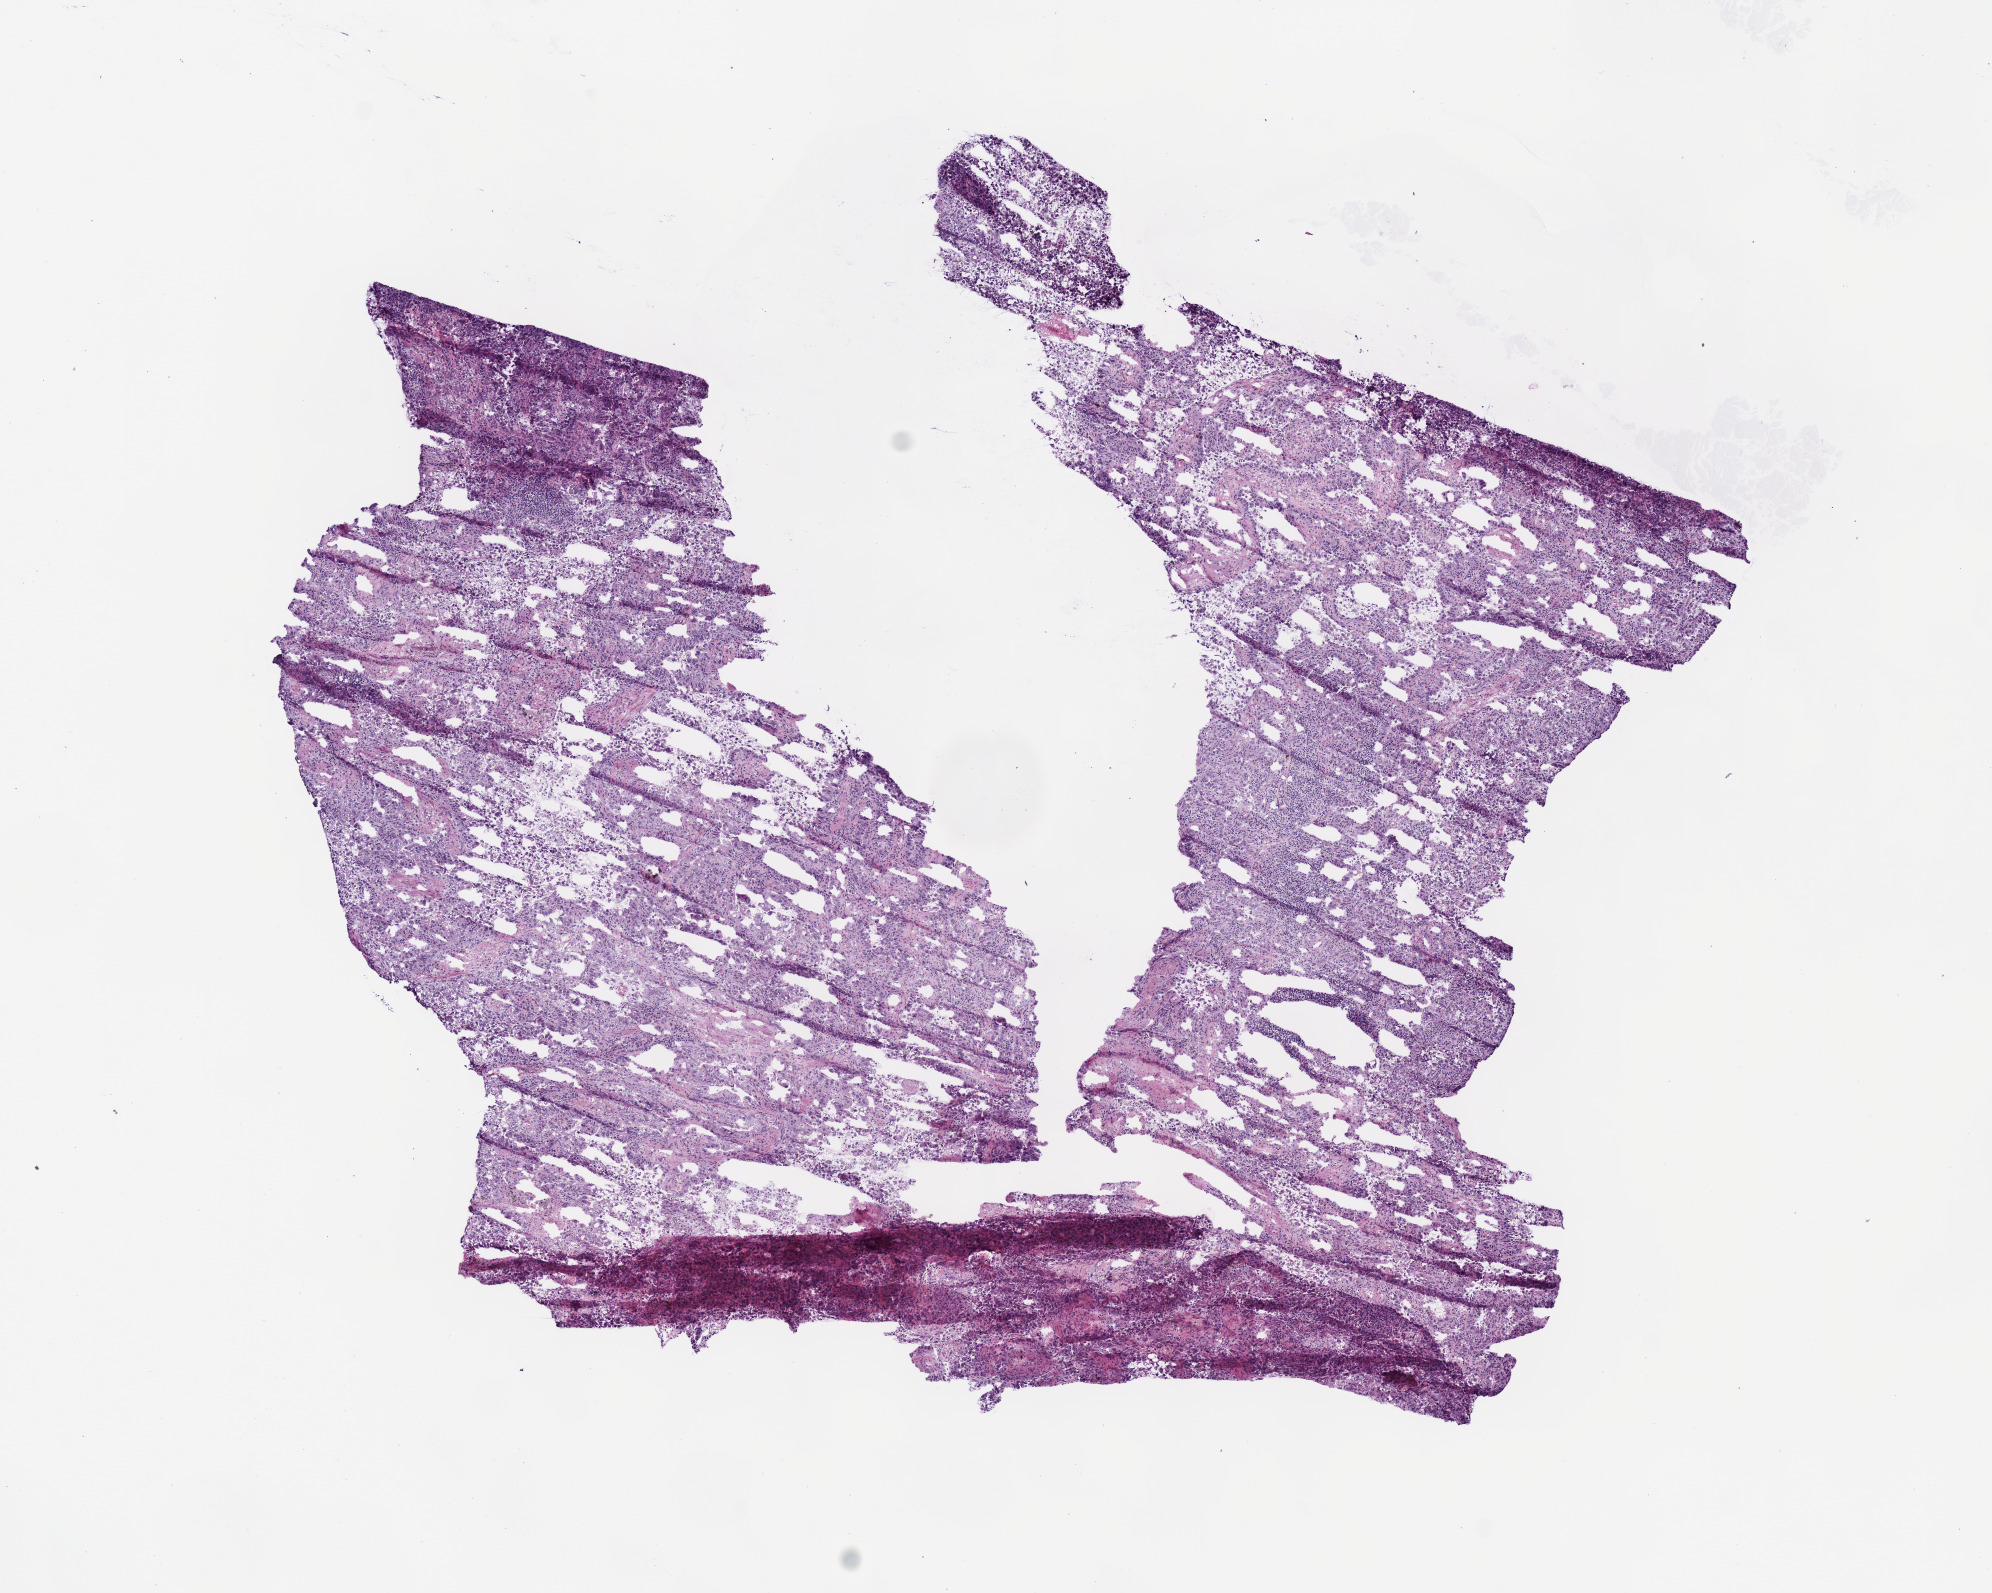
Whole-slide histology image, Hematoxylin and eosin (H&E) stained — low-resolution overview of the scanned area, about 7.8 x 6.3 mm; frozen section from the bottom of the tissue portion; lung, primary tumour sample. Male, age 62 years at initial diagnosis. Slide review estimates, as recorded: tumour cells 100%, tumour nuclei 61%, normal cells 0%, stromal cells 0%, necrosis 0%. Inflammatory infiltration, as recorded: lymphocyte infiltration 20%, monocyte infiltration 5%, neutrophil infiltration 5%.
Diagnosis: Adenocarcinoma, NOS (upper lobe, lung). AJCC pathologic stage: IIB (7th edition). Laterality: right.